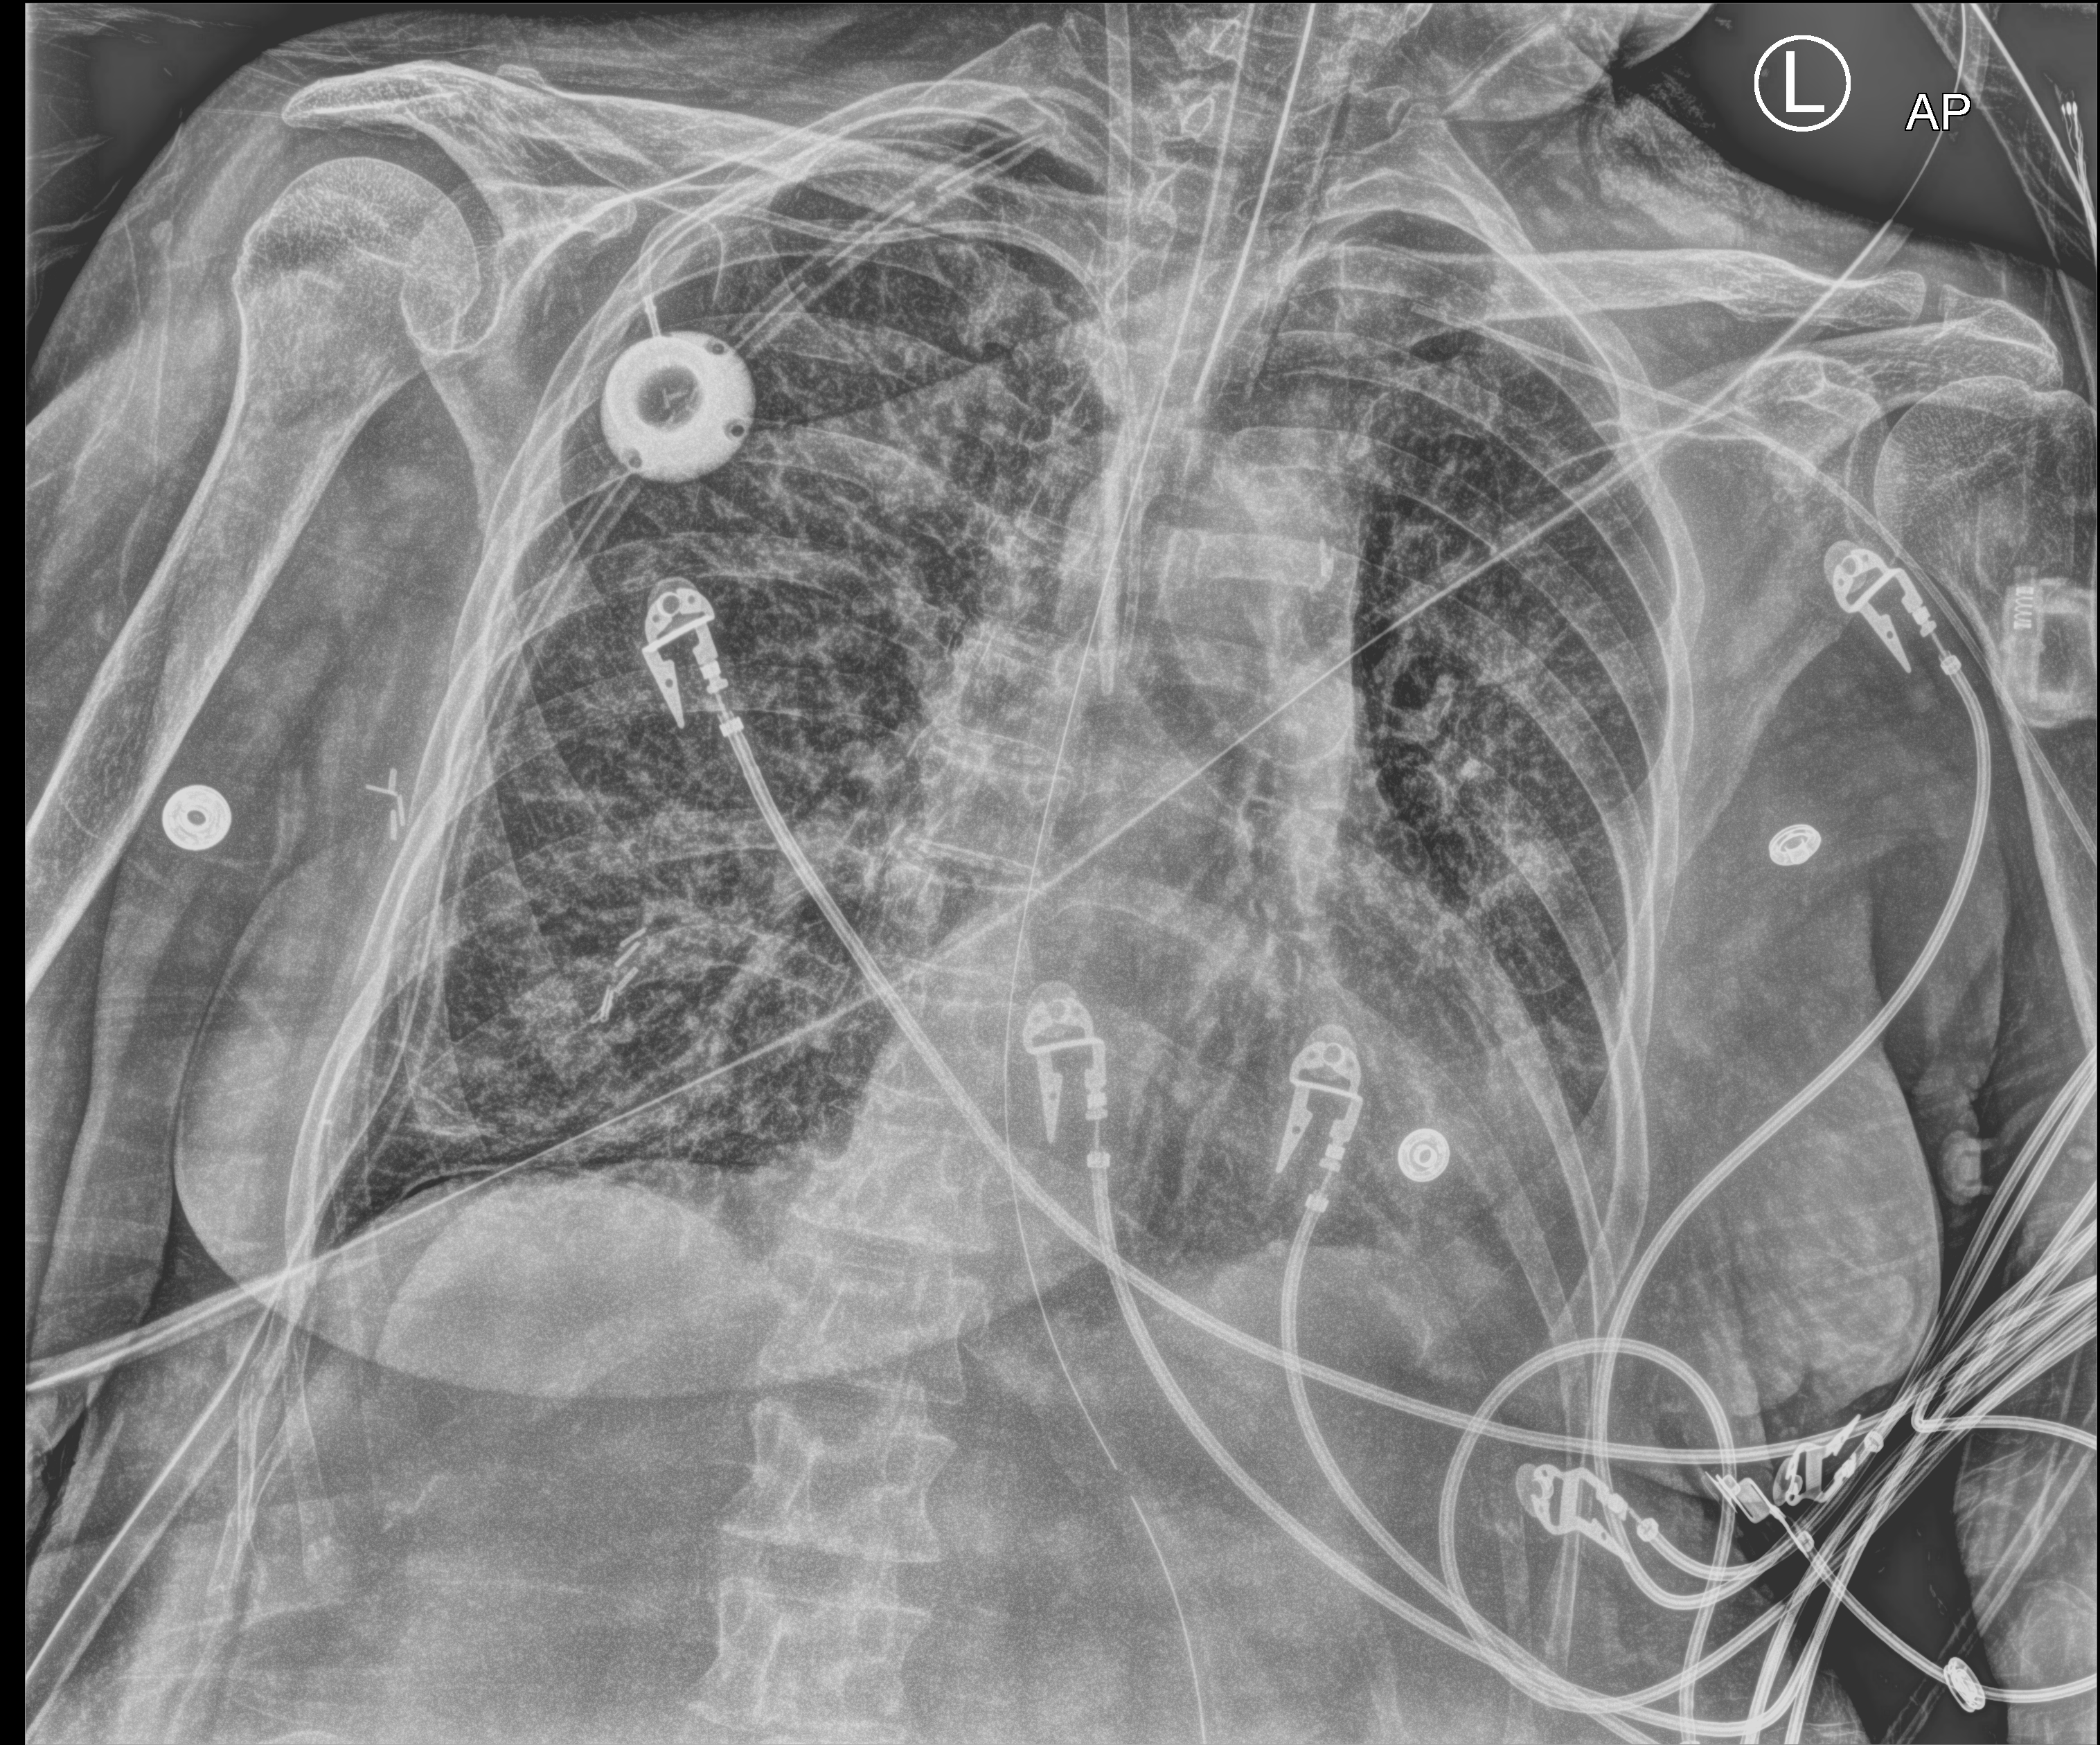
Portable chest radiograph; anteroposterior (AP) projection. Female patient hospitalised with COVID-19, age 60–74 years.
Hospital-stay facts (about this admission, not read from this image; timing relative to this image not recorded): mechanically ventilated during this hospital stay: yes; admitted to intensive care during this hospital stay: yes.